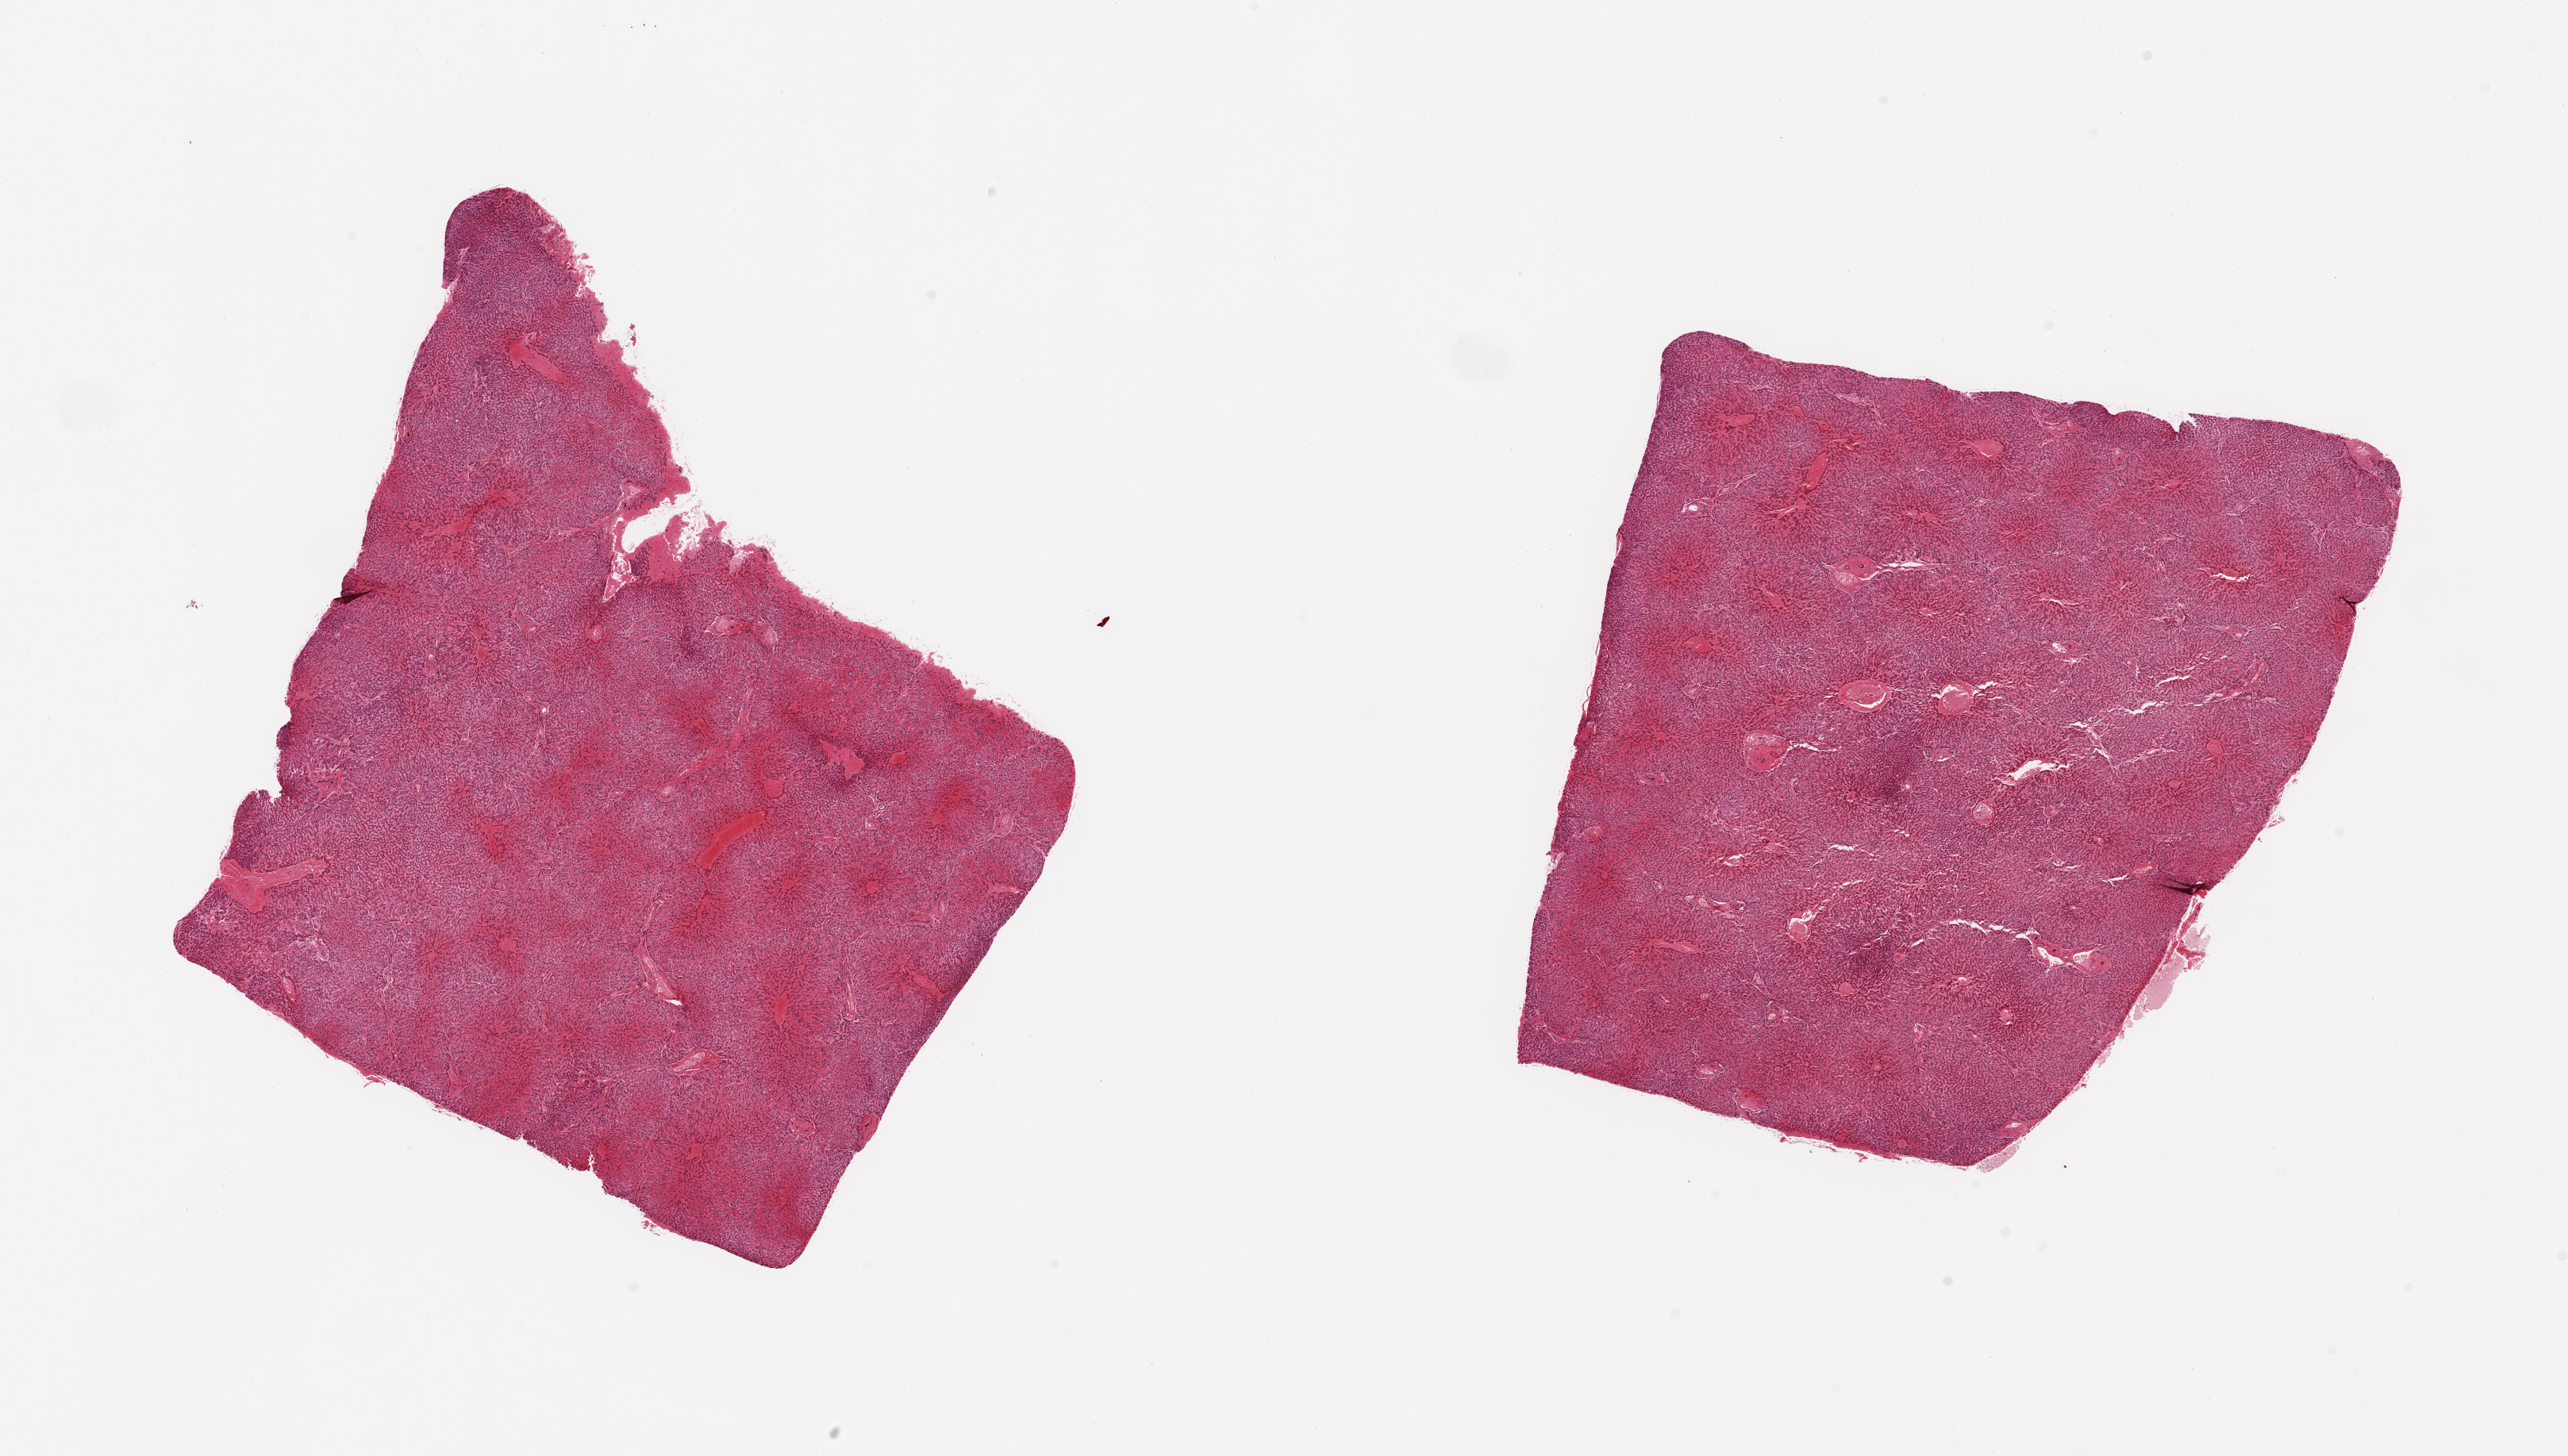
Digitized hematoxylin and eosin (H&E)-stained section — a low-resolution overview of the entire scanned area, about 25.6 x 14.5 mm (slide scanned at 20x); PAXgene-fixed, paraffin-embedded tissue; section of liver (target tissue); tissue donor sample. Donor sex: female.
Reviewer comment on this tissue sample: 2 pieces; moderate central passive congestion.